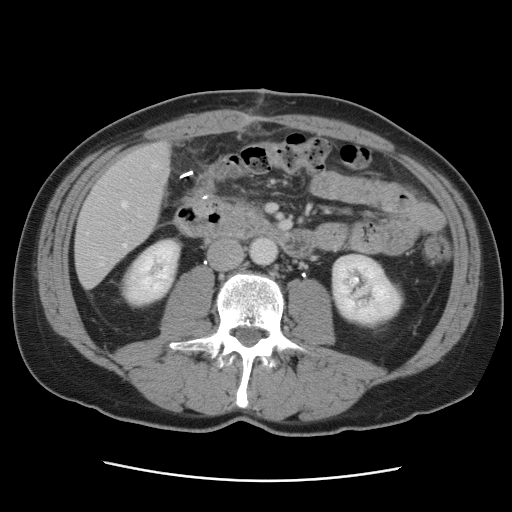
Contrast-enhanced abdominal CT, one axial slice. Position 23 of 89 along the scan axis. Intravenous contrast given. Soft-tissue window (W 400 / L 40 HU). 512 × 512 image matrix, field of view 366 × 366 mm. Male patient, age 59 years. Case-level facts recorded for this patient, not image findings: diagnosis: colorectal cancer liver metastases, imaged before liver resection; multiple liver metastases: yes; largest metastasis: 0.6 cm; disease in both lobes: yes.
Annotated regions visible in this slice (outlined manually by an expert reader):
- hepatic veins: box from (x=87, y=164) to (x=159, y=266) px
- liver: (x=77, y=144)–(x=170, y=287)
- planned liver remnant (the part of the liver to remain after resection): (x=77, y=144)–(x=170, y=250)
- portal vein (with intrahepatic branches): (x=123, y=227)–(x=126, y=230)